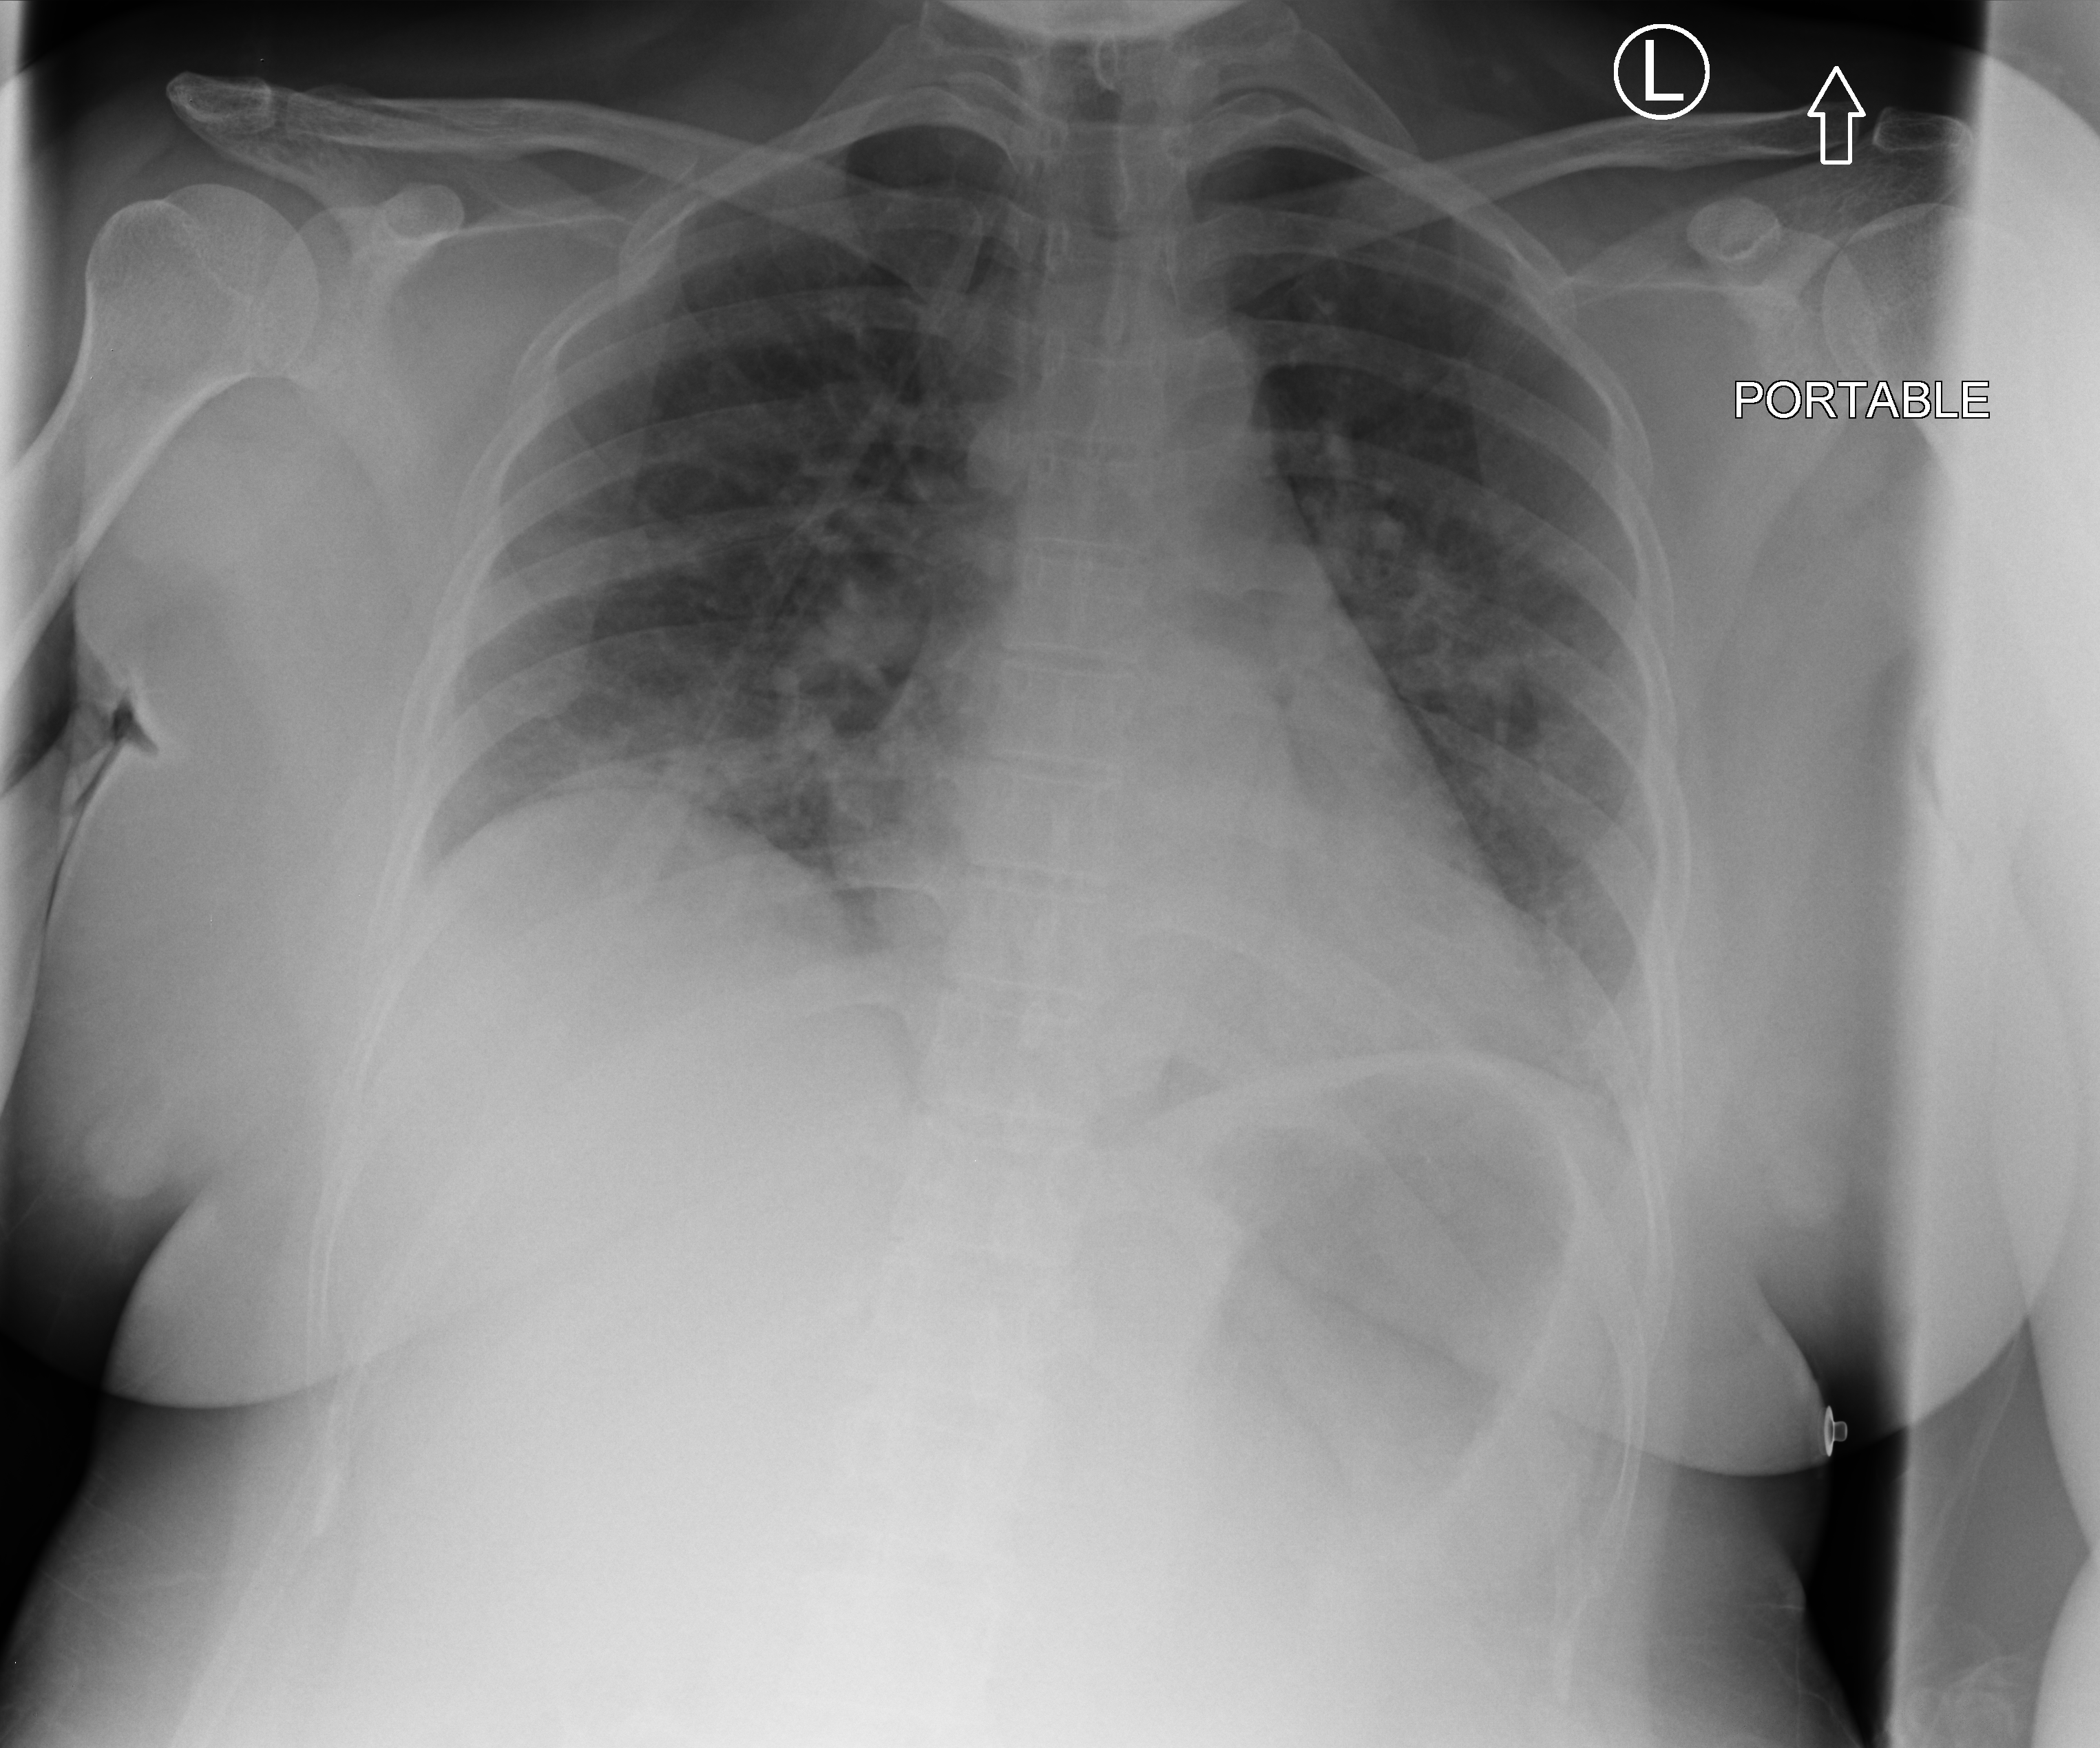
Bedside chest radiograph (computed radiography); anteroposterior (AP) projection. Patient hospitalised with COVID-19; female, aged 18–59 years.
From the hospital-stay record, not from the radiograph (when in the stay this image was taken is not recorded):
- mechanically ventilated during this hospital stay: no